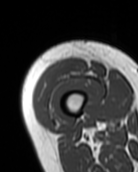
MRI of an extremity soft-tissue mass, one axial slice. Position 13 of 99 along the scan axis. MR volume resampled by the dataset authors to the PET/CT grid (not the native acquisition matrix). 138 × 172 image matrix, field of view 135 × 168 mm. Female patient. Case-level facts recorded for this patient, not image findings: histological type: pleiomorphic undifferentiated sarcoma; grade: high; site of the primary tumour: right quadricep.
Outlined on this slice (expert contour drawn on MRI and transferred to this co-registered scan by the dataset authors):
- gross tumour volume including surrounding oedema: bounding box [x1, y1, x2, y2] px = [35, 59, 86, 110]